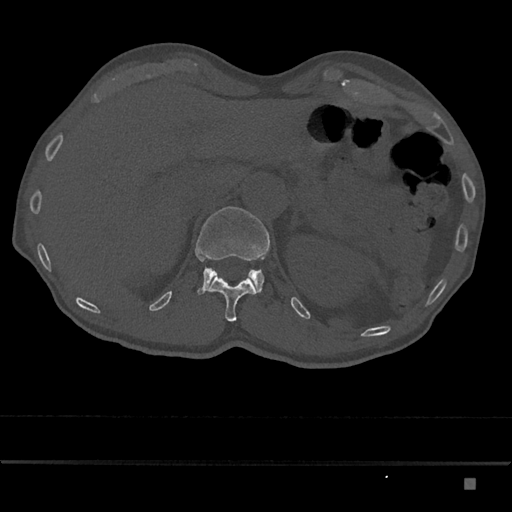
CT including the spine, one axial slice. Position 582 of 797 along the scan axis. 120 kVp. Bone window (W 1800 / L 400 HU). 512 × 512 image matrix. Patient: male, 72 years. From the clinical record (not read from this slice): primary cancer: prostate.
Annotated regions visible in this slice (semi-automatic segmentation, software-assisted and operator-edited):
- L1 vertebra: box from (x=195, y=206) to (x=270, y=295) px
- T12 vertebra: (x=203, y=275)–(x=256, y=322)